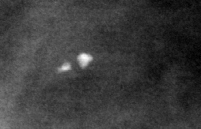
Crop from a digitized film mammogram around one marked abnormality, right breast, MLO view.
Calcifications, morphology round and regular / lucent center / punctate, distribution diffusely scattered; BI-RADS assessment category 2; subtlety rating 5 on a 1 (subtle) to 5 (obvious) scale; benign; no additional work-up was recommended (benign without callback).